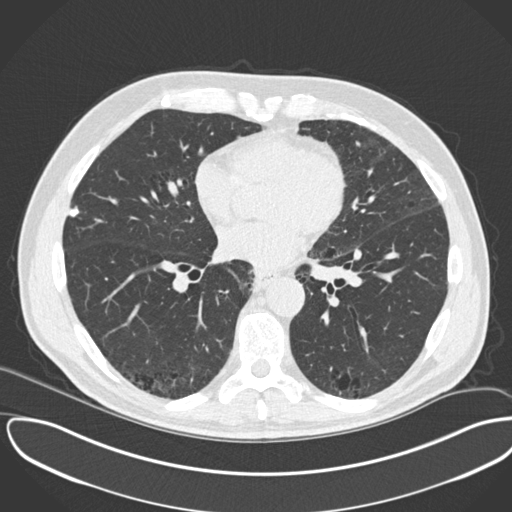
Low-dose screening chest CT, one axial slice; slice 111 of 245 in the series (ordered by position); 120 kVp; lung window (W 1500 / L -600 HU); 512 × 512 image matrix, field of view 396 × 396 mm.
Outlined on this slice (outlined manually by an expert reader):
- lesion 1 (tumor, upper lobe of right lung): box from (x=70, y=209) to (x=79, y=218) px